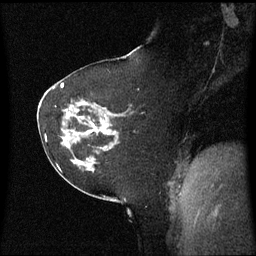
Breast MRI (dynamic contrast-enhanced), one sagittal slice; position 32 of 60 along the scan axis; dynamic contrast-enhanced series, image 2 of 3 at this slice position (ordered by acquisition); 1.5 T; TE 4.2 ms, TR 8.4 ms; 2.2 mm slice thickness; 256 × 256 image matrix, field of view 220 × 220 mm. Patient: female, 60 years. From the clinical record (not read from this slice): setting: breast cancer imaged before/during neoadjuvant chemotherapy; receptor status: triple-negative.
Structures marked on this image (semi-automatic segmentation, software-assisted and operator-edited):
- analysis volume of interest (the breast-tissue region the enhancement analysis was run in; not a lesion): box from (x=62, y=100) to (x=126, y=161) px
- tumour enhancement mask (voxels above the 70 % enhancement threshold inside the analysis volume of interest): (x=93, y=126)–(x=106, y=147)